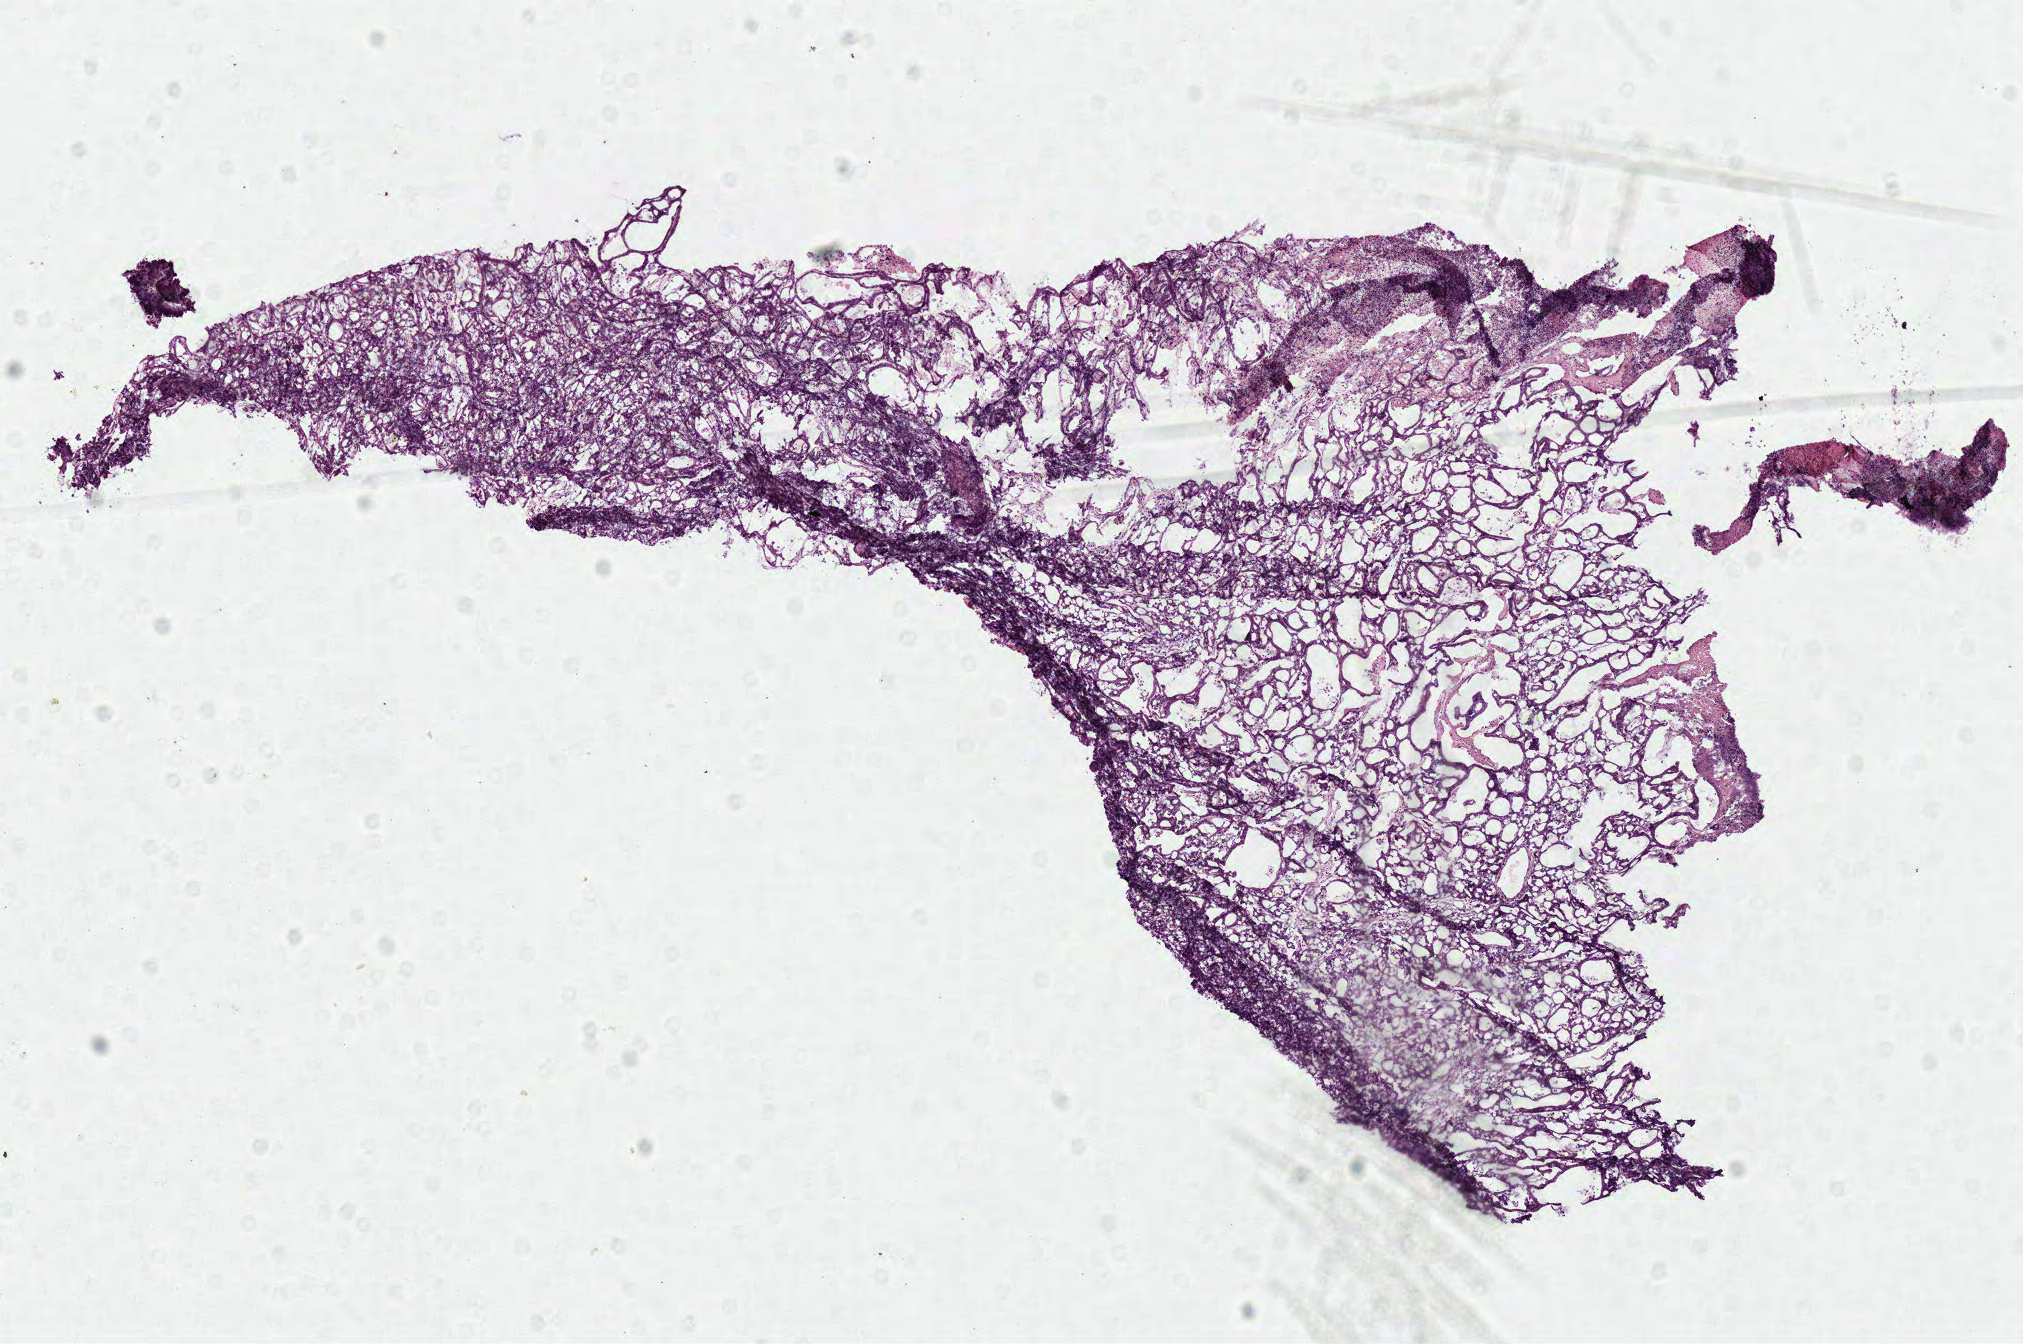
Hematoxylin and eosin (H&E) stained whole-slide image, shown as a low-resolution overview of the whole scanned area (about 8.0 x 5.3 mm), frozen section from the top of the tissue portion, colon, primary tumour sample. Female, age 73 years at initial diagnosis. Slide review estimates, as recorded: tumour cells 90%, tumour nuclei 80%, normal cells 0%, stromal cells 10%, necrosis 0%.
AJCC pathologic stage: IIA. Lymph nodes positive (case pathology): 0 of 17 examined. Histologic diagnosis: Adenocarcinoma, NOS (ascending colon).